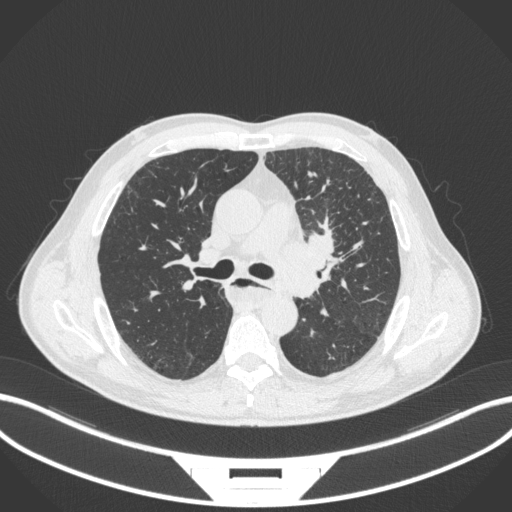
Chest CT, one axial slice; position 236 of 411 along the scan axis; reconstruction kernel B31f; 120 kVp; lung window (W 1500 / L -600 HU); 512 × 512 image matrix, field of view 400 × 400 mm. Male patient, age 57 years. Case-level facts recorded for this patient, not image findings: clinical TNM (as recorded): T2a N1 M0.
Outlined on this slice (rectangle marked by the reading radiologist):
- lung tumour (recorded histology: squamous cell carcinoma): box from (x=276, y=224) to (x=337, y=275) px